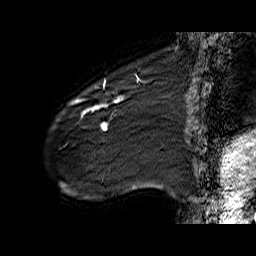
Breast MRI (dynamic contrast-enhanced), one sagittal slice. Dynamic contrast-enhanced series, time point 2 of 6 at this slice position (early post-contrast). 1.5 T. TE 6.4 ms, TR 32.9 ms. 4 mm slice thickness. 256 × 256 image matrix, field of view 200 × 200 mm. Female patient. From the clinical record (not read from this slice): setting: breast cancer imaged before/during neoadjuvant chemotherapy; receptor status: HER2-positive.
Structures marked on this image (semi-automatically segmented with operator editing):
- analysis volume of interest (the breast-tissue region the enhancement analysis was run in; not a lesion): bounding box <61,77,141,142> (left, top, right, bottom; pixels)
- tumour enhancement mask (voxels above the 100 % enhancement threshold inside the analysis volume of interest): <70,79,139,130>